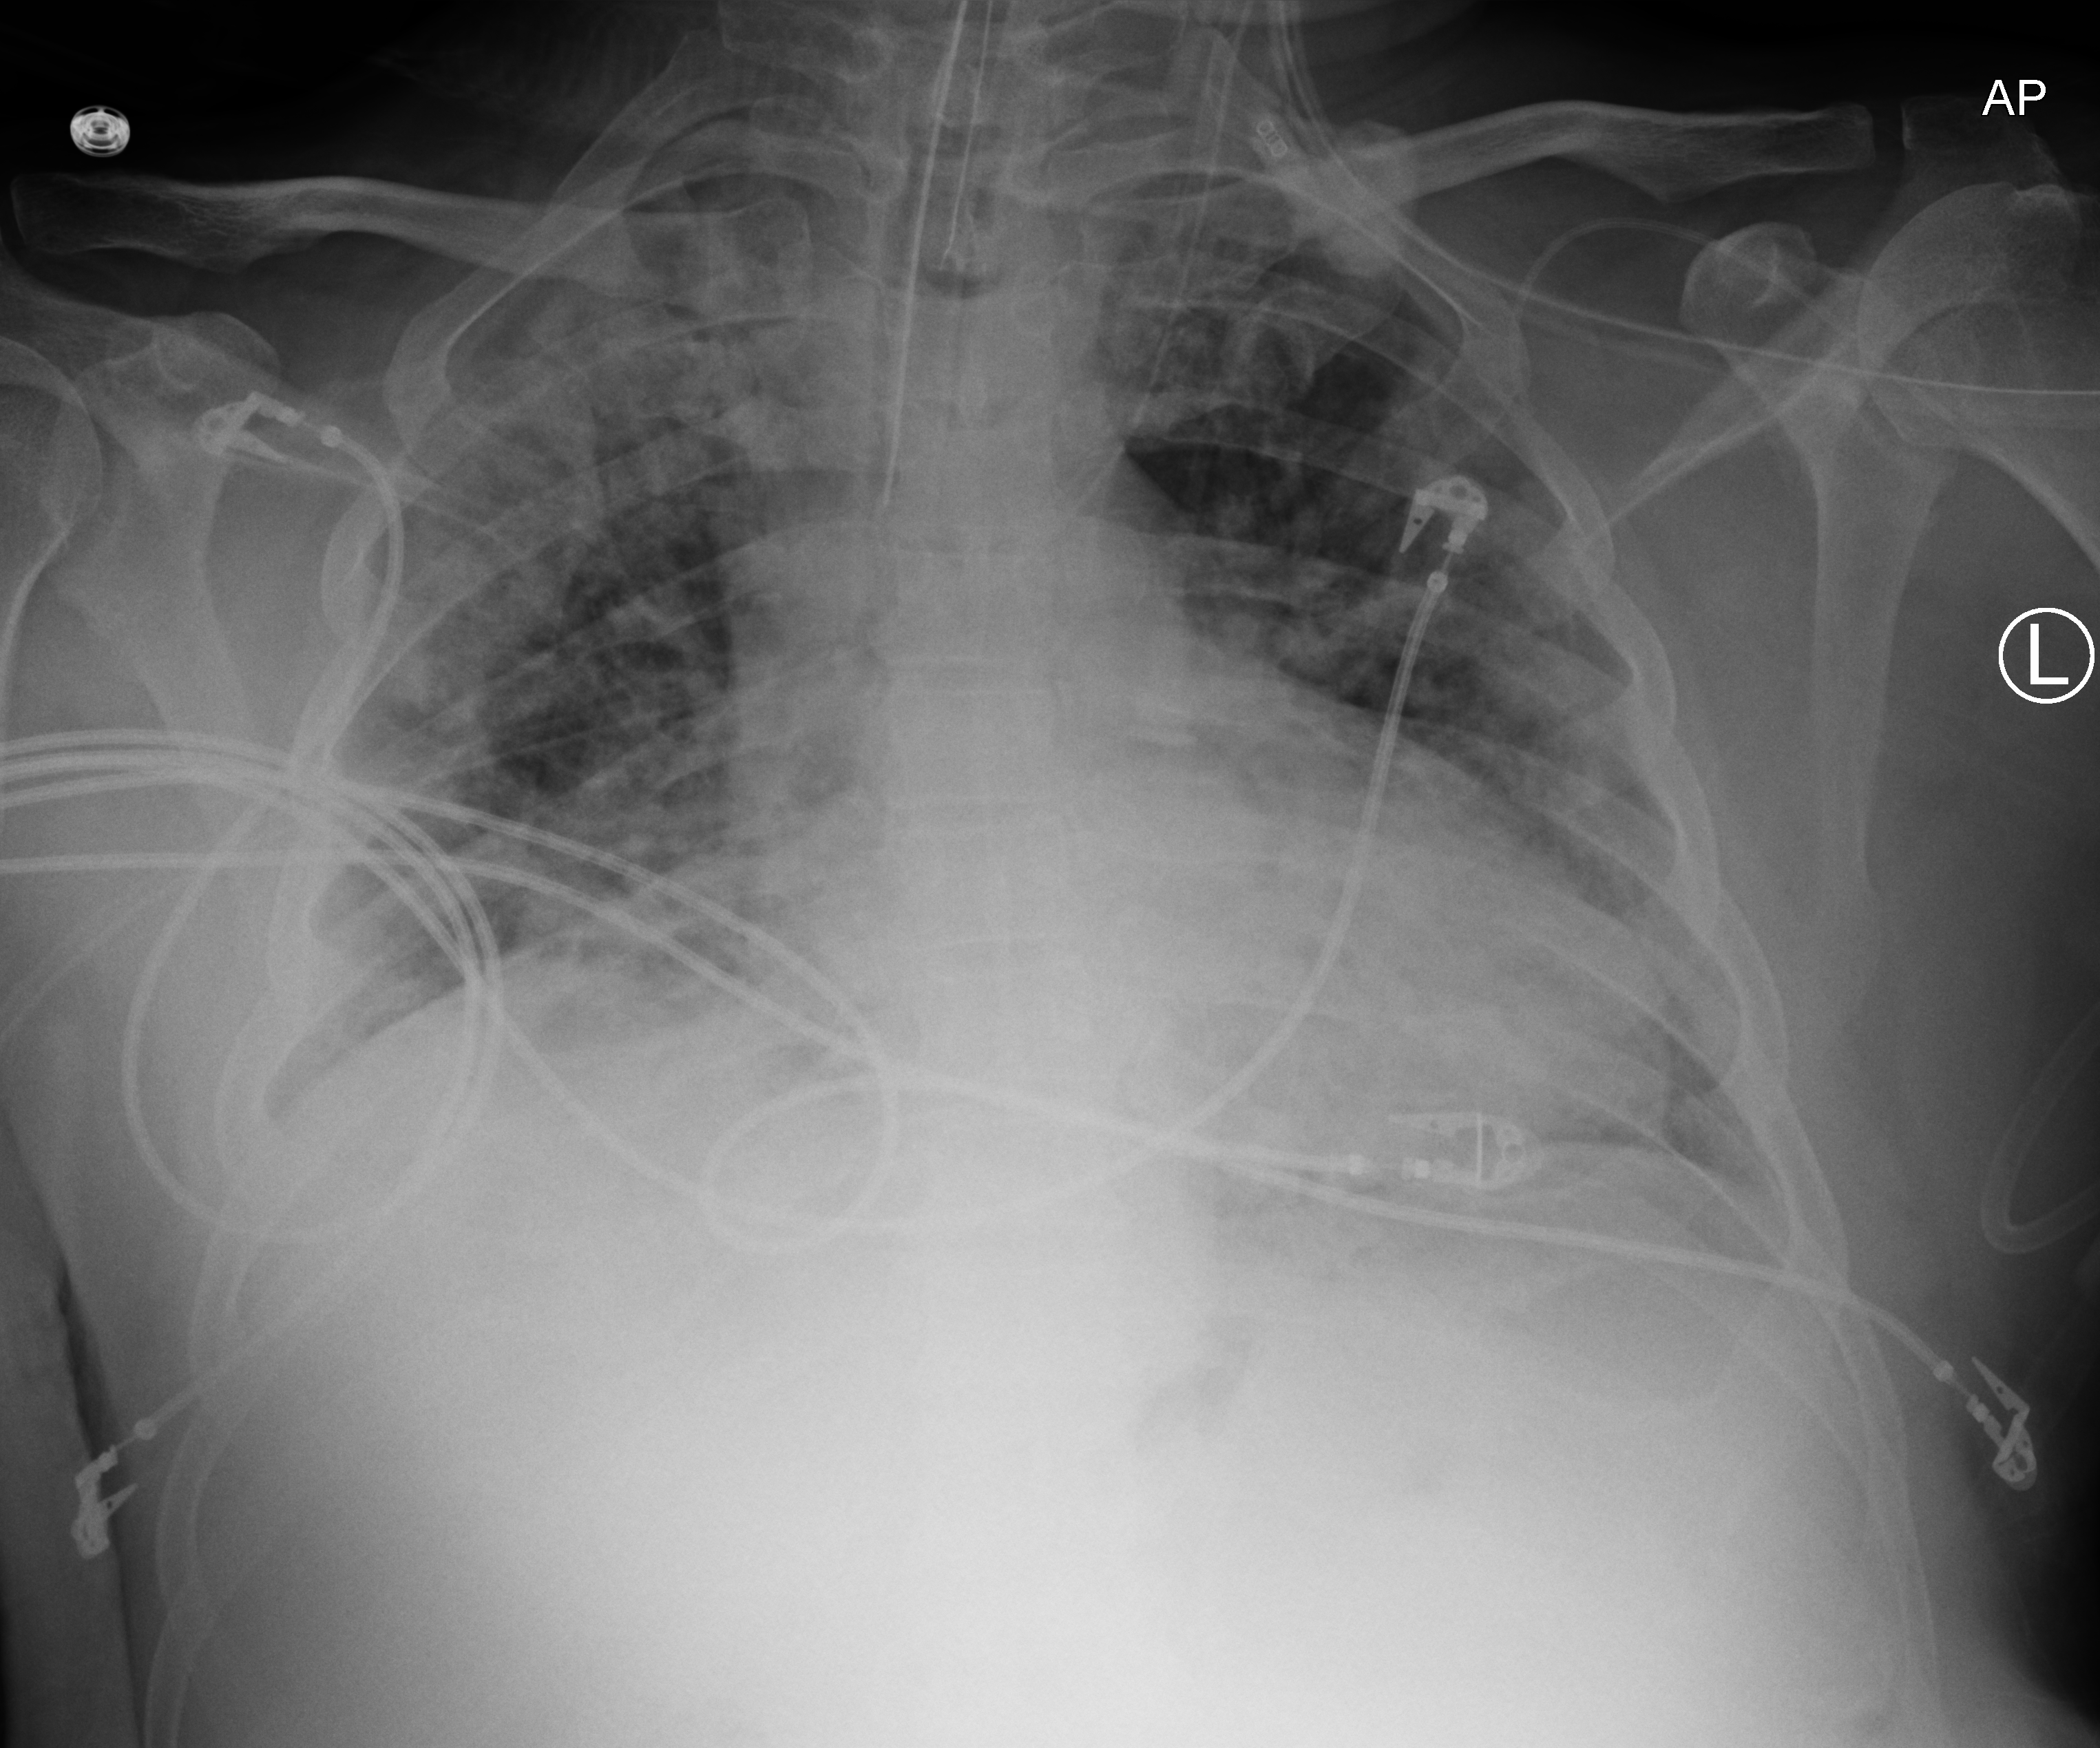
Portable chest radiograph; anteroposterior (AP) projection. Patient hospitalised with COVID-19; male, aged 18–59 years.
Admission-level facts for this patient (not findings on this image; timing relative to this image not recorded):
- admitted to intensive care during this hospital stay: no
- length of hospital stay: 32 days